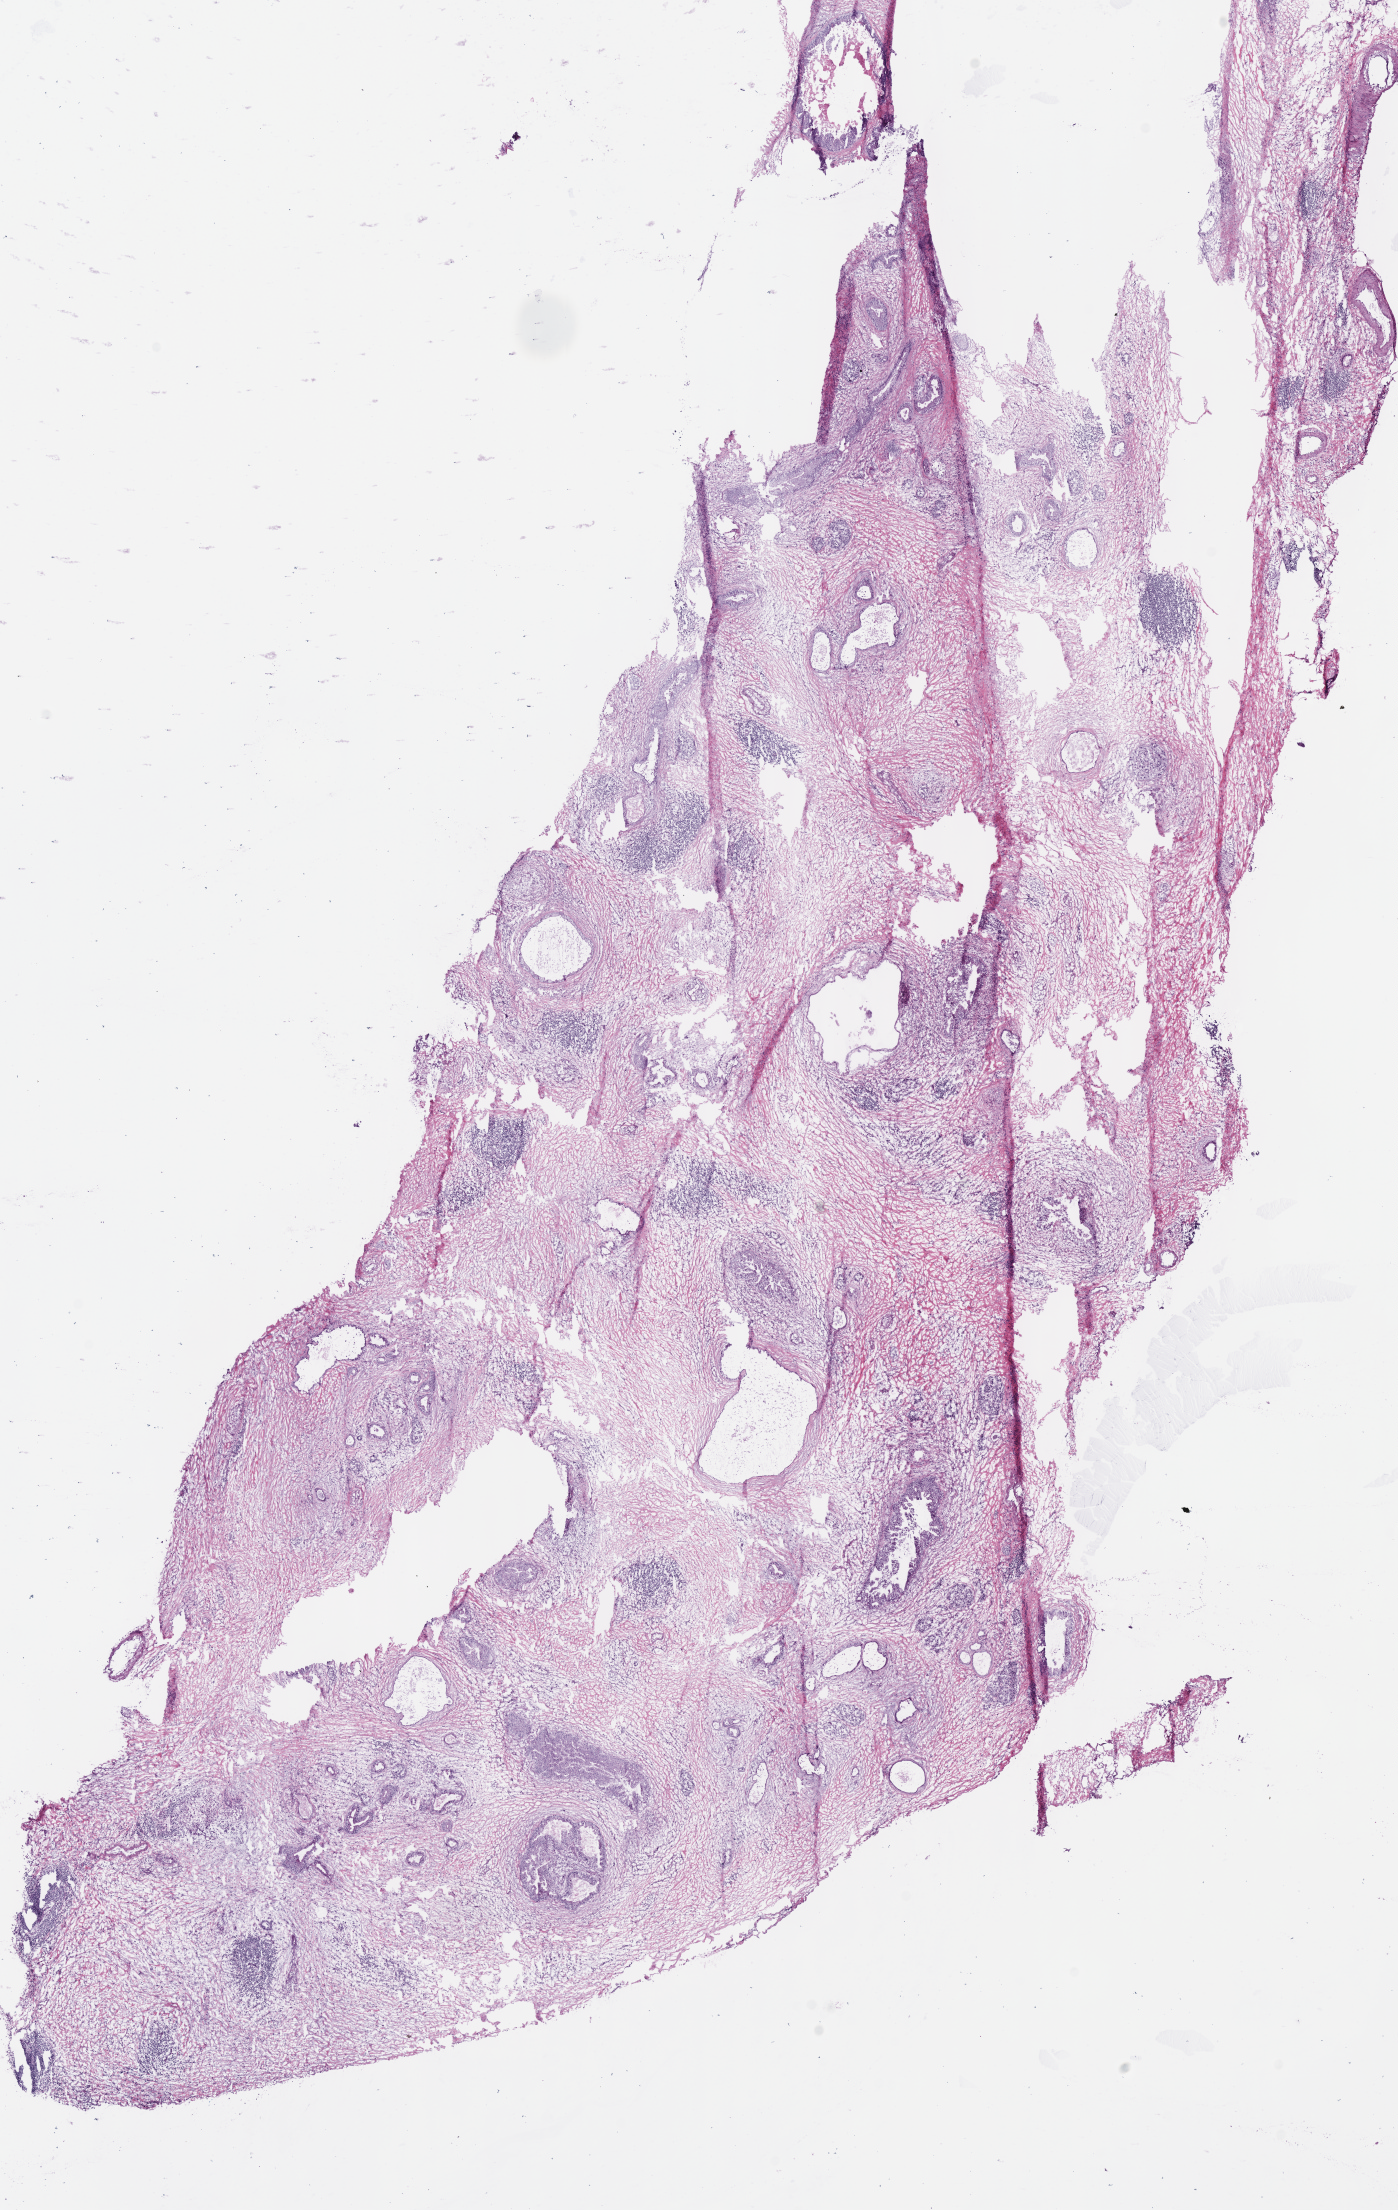
Whole-slide histology image, H&E-stained — whole scanned area (about 11.0 x 17.4 mm, from a 40x scan) shown as a low-resolution overview. Frozen section from the bottom of the tissue portion. Pancreas, primary tumour sample. Patient: female, age at initial diagnosis 66 years. Histologic grade: G2 (moderately differentiated). Pathologist review of this section (percent, as recorded): tumour cells 60%, tumour nuclei 50%, normal cells 0%, stromal cells 40%, necrosis 0%.
AJCC pathologic stage: IIA (6th edition). Lymph nodes positive (case pathology): 0 of 12 examined. Pathologic diagnosis: Infiltrating duct carcinoma, NOS.